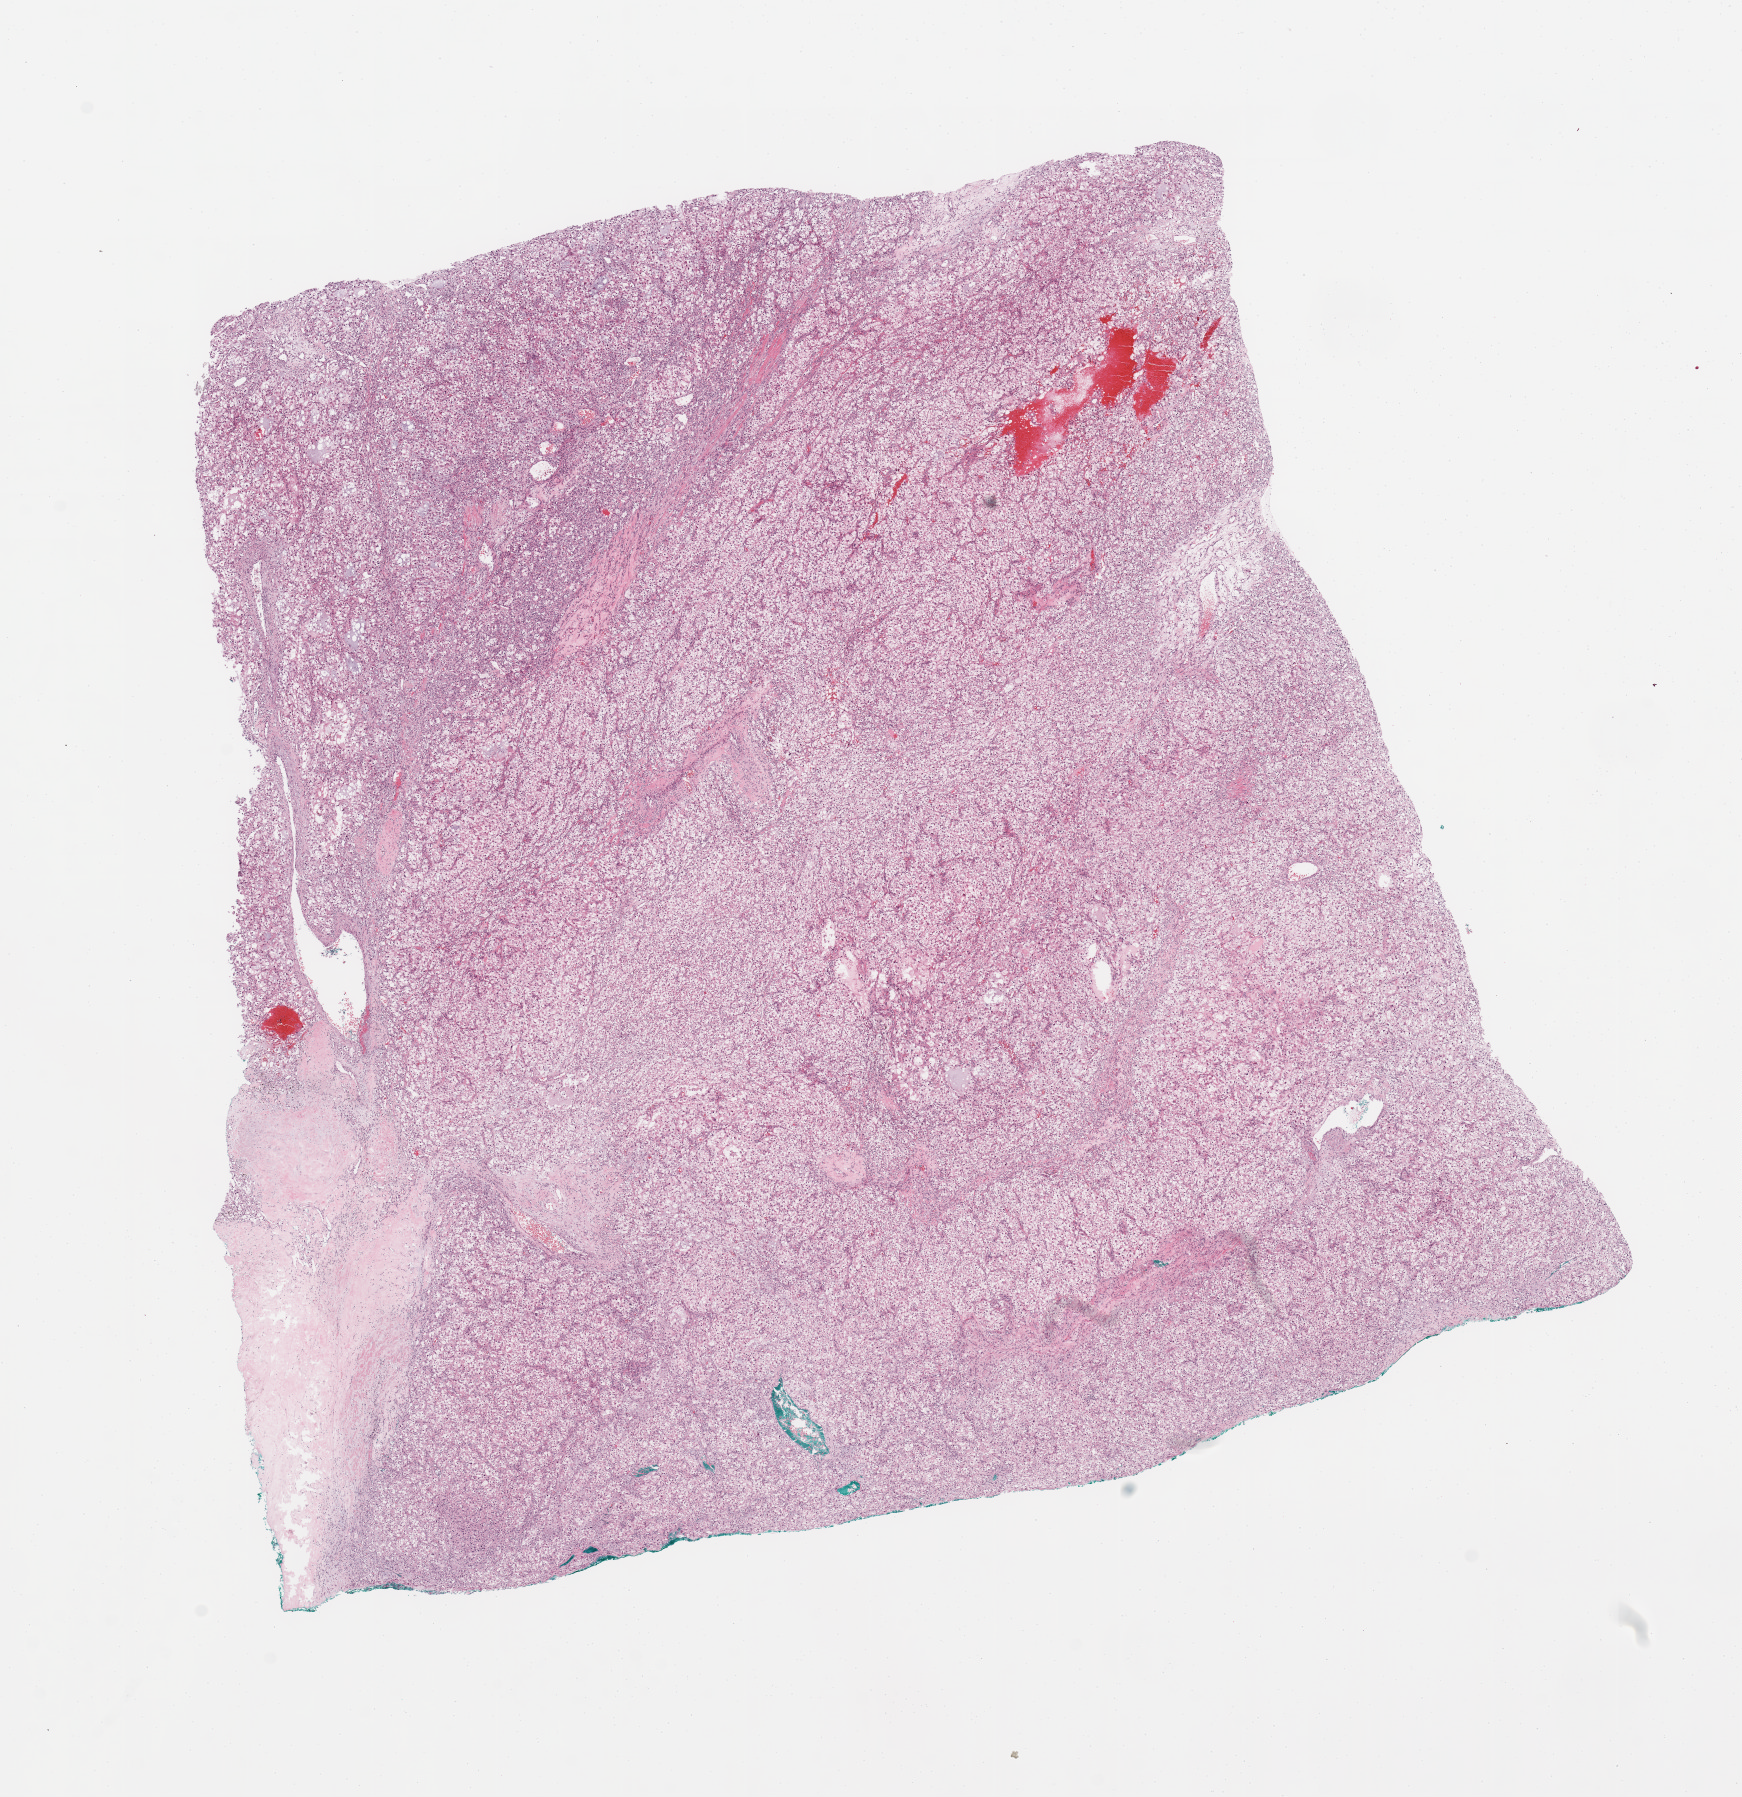
H&E whole-slide image, low-resolution overview of the scanned area, about 13.8 x 14.2 mm (from a 20x scan); tumour tissue sample, kidney. 70-year-old male patient. Histologic grade: G3 (poorly differentiated).
* primary tumour site (as recorded): middle
* AJCC pathologic stage: II
* histologic diagnosis: Renal cell carcinoma, NOS